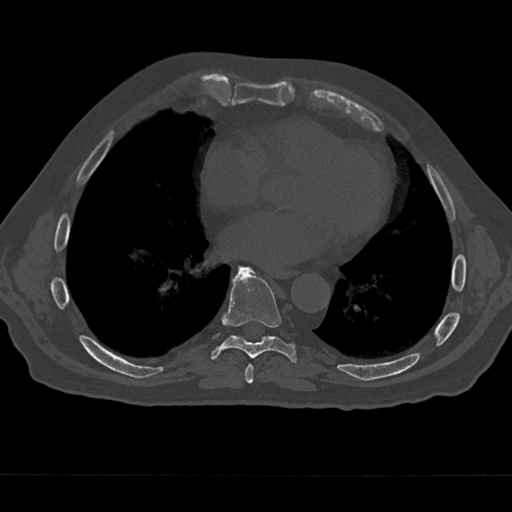
CT including the spine, one axial slice. Slice 314 of 797 in the series (ordered by position). 120 kVp. Bone window (W 1800 / L 400 HU). 0.5 mm slice thickness. 512 × 512 image matrix. Patient: male, 75 years. From the clinical record (not read from this slice): primary cancer: renal; vertebrae with lytic lesions (as recorded): T4.
Structures marked on this image (semi-automatically segmented with operator editing):
- T7 vertebra: bounding box [x1, y1, x2, y2] px = [240, 363, 259, 384]
- T8 vertebra: [210, 267, 297, 363]